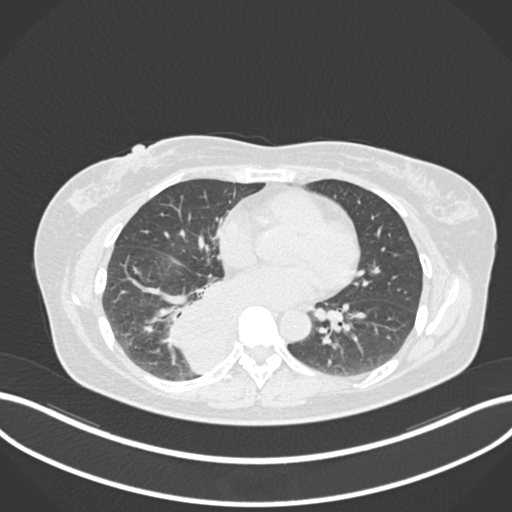
Chest CT, one axial slice. Slice 572 of 677 in the series (ordered by position). Lung window (W 1500 / L -600 HU). 1 mm slice thickness. 512 × 512 image matrix, field of view 400 × 400 mm. Female patient, age 54 years. Case-level facts recorded for this patient, not image findings: clinical TNM (as recorded): T4 N0 M0.
Annotated regions visible in this slice (bounding box drawn by a radiologist):
- lung tumour (recorded histology: adenocarcinoma): bounding box <166,278,253,376> (left, top, right, bottom; pixels)